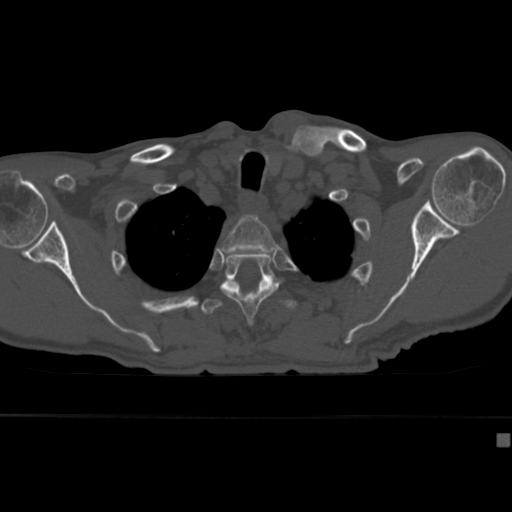
CT including the spine, one axial slice. Position 333 of 430 along the scan axis. 120 kVp. Bone window (W 1800 / L 400 HU). 1.5 mm slice thickness. 512 × 512 image matrix, field of view 337 × 337 mm. Male patient, age 64 years. From the clinical record (not read from this slice): primary cancer: uterus.
Annotated regions visible in this slice (semi-automatic segmentation, software-assisted and operator-edited):
- T2 vertebra: bounding box <221,215,276,258> (left, top, right, bottom; pixels)
- T3 vertebra: <220,252,280,325>
- T4 vertebra: <200,290,297,315>